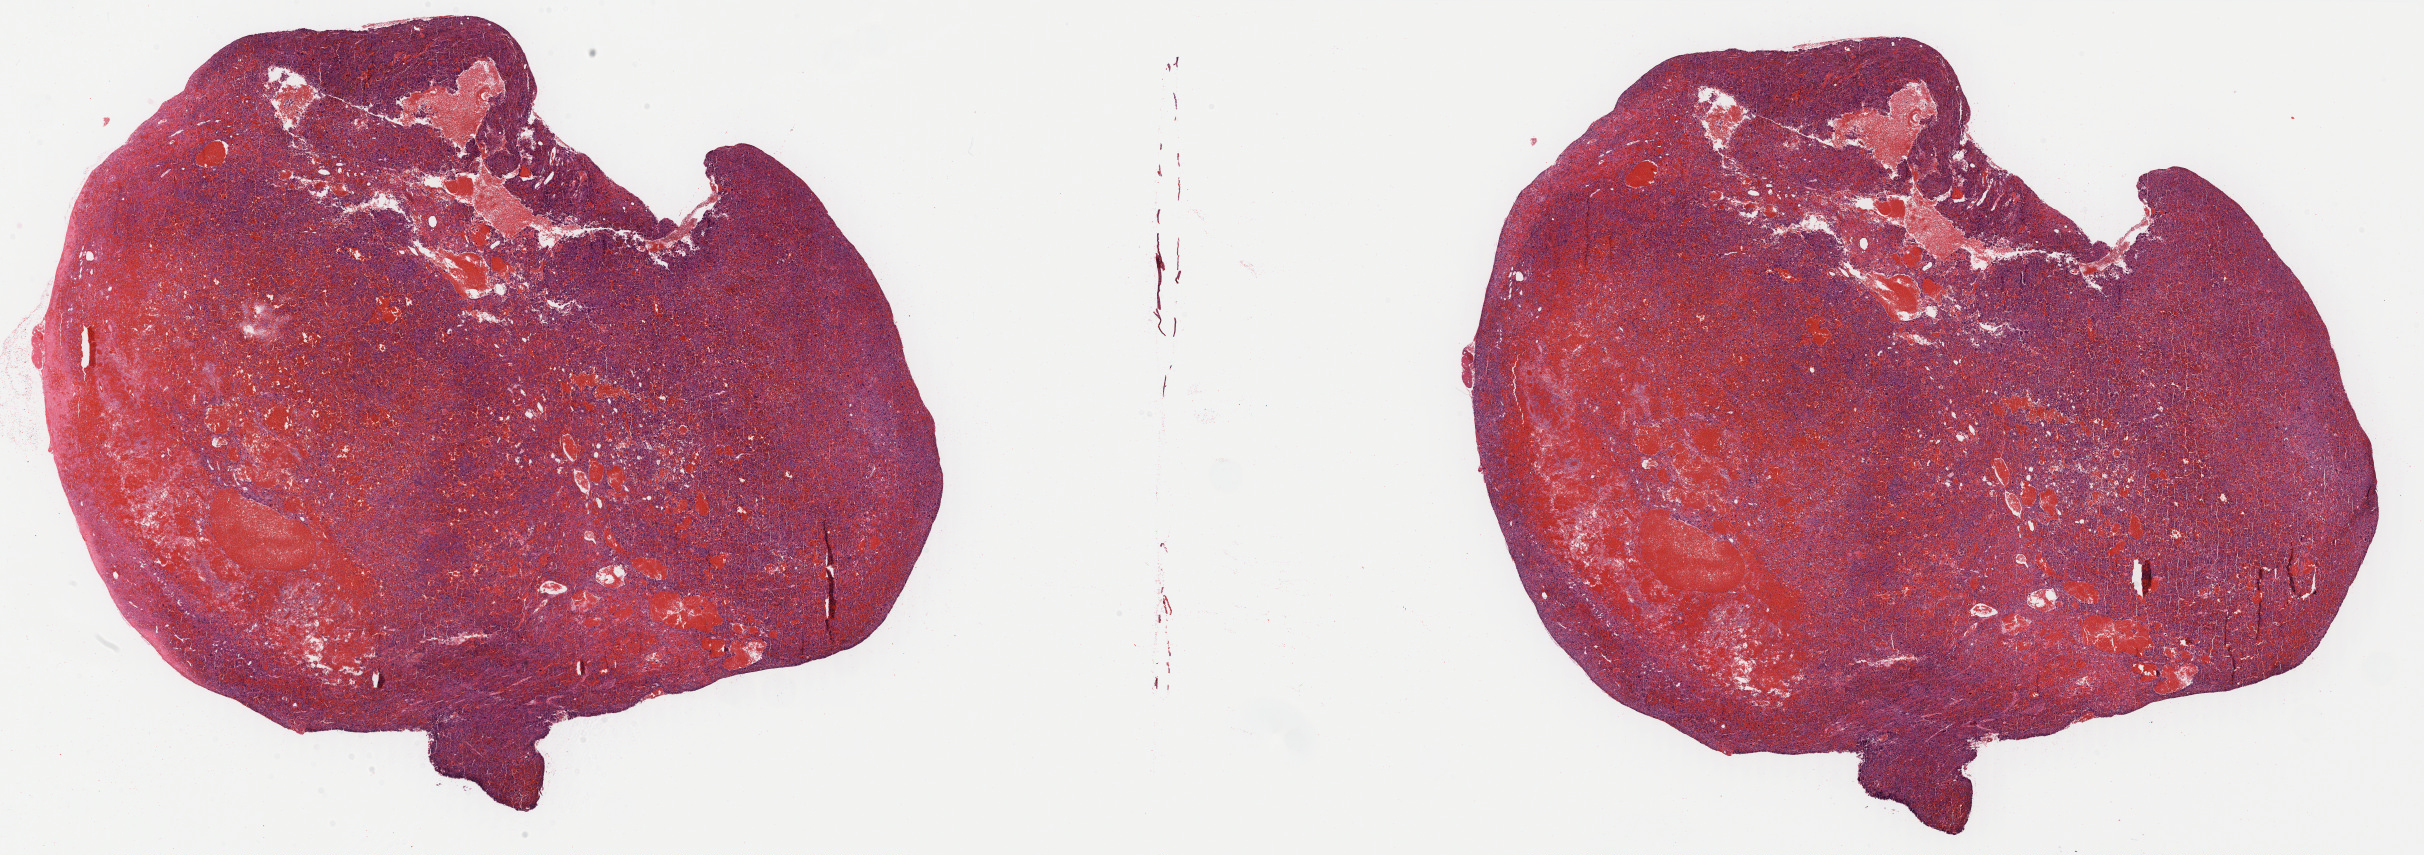
H&E-stained whole-slide image — a low-resolution overview of the entire scanned area, about 38.4 x 13.5 mm, formalin-fixed paraffin-embedded (FFPE) diagnostic section, primary tumour sample from the connective, subcutaneous and other soft tissues. Female, age 78 years at initial diagnosis.
* histologic diagnosis: Undifferentiated sarcoma